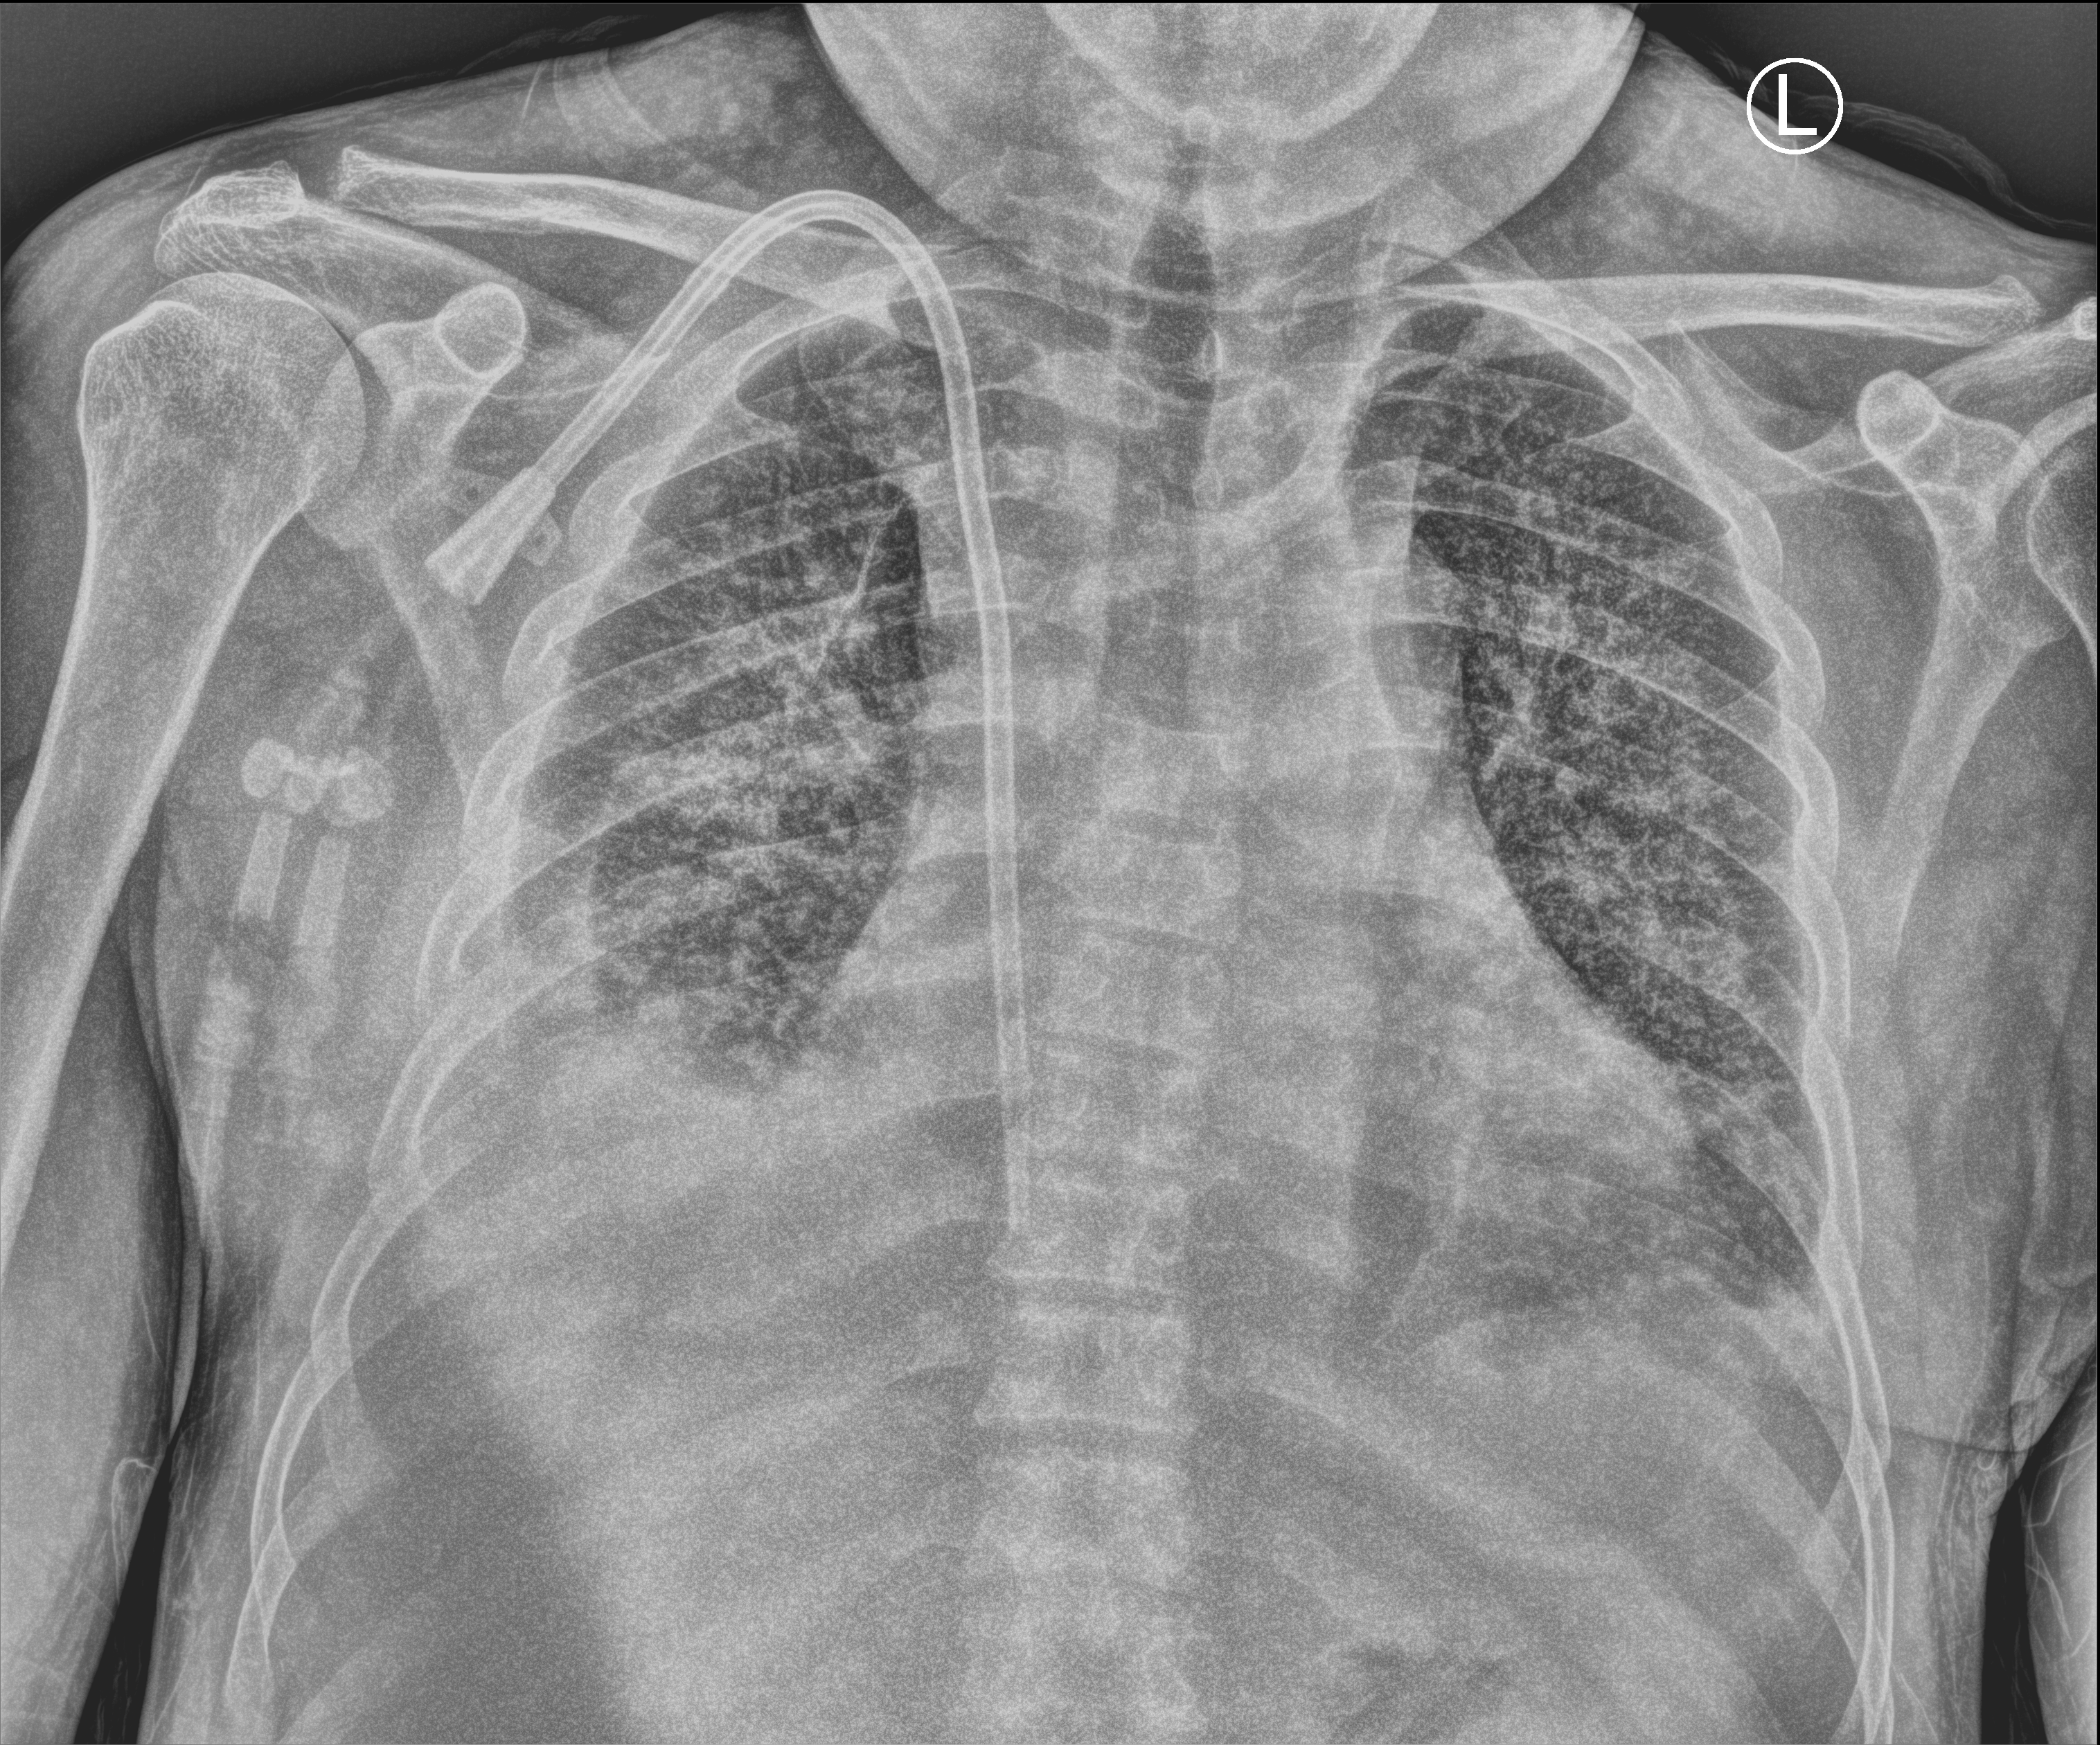
Chest X-ray (portable). Male patient hospitalised with COVID-19, age 18–59 years.
From the hospital-stay record, not from the radiograph (when in the stay this image was taken is not recorded): mechanically ventilated during this hospital stay: no.